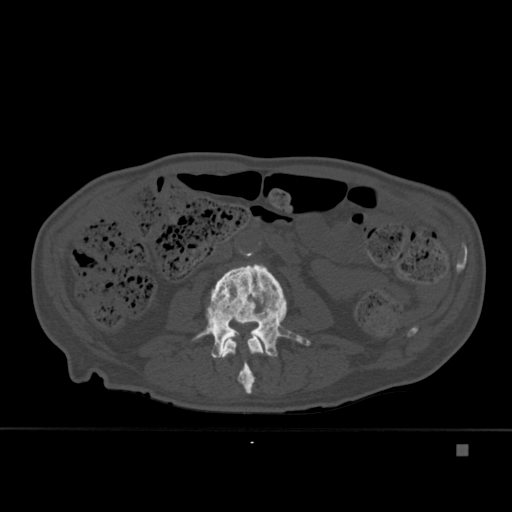
CT including the spine, one axial slice; position 147 of 451 along the scan axis; bone window (W 1800 / L 400 HU); 1.5 mm slice thickness; 512 × 512 image matrix, field of view 378 × 378 mm. Male patient, age 75 years. Case-level facts recorded for this patient, not image findings: primary cancer: prostate.
Outlined on this slice (semi-automatically segmented with operator editing):
- L2 vertebra: box from (x=221, y=334) to (x=264, y=394) px
- L3 vertebra: (x=192, y=264)–(x=311, y=377)